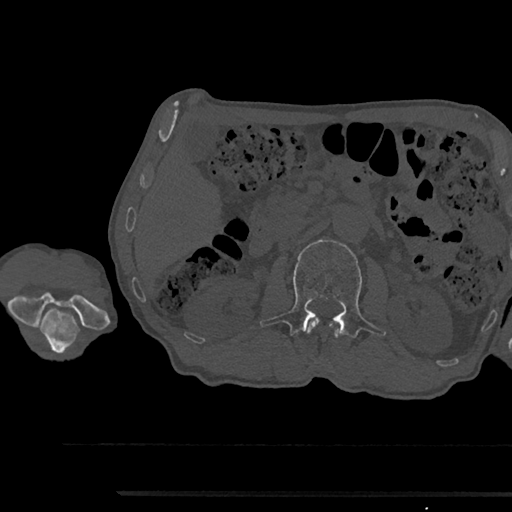
CT including the spine, one axial slice. 120 kVp. Bone window (W 1800 / L 400 HU). 512 × 512 image matrix, field of view 367 × 367 mm. Patient: male, 79 years. Case-level facts recorded for this patient, not image findings: primary cancer: prostate.
Structures marked on this image (semi-automatic segmentation, software-assisted and operator-edited):
- L1 vertebra: box from (x=308, y=319) to (x=341, y=340) px
- L2 vertebra: (x=260, y=240)–(x=386, y=360)